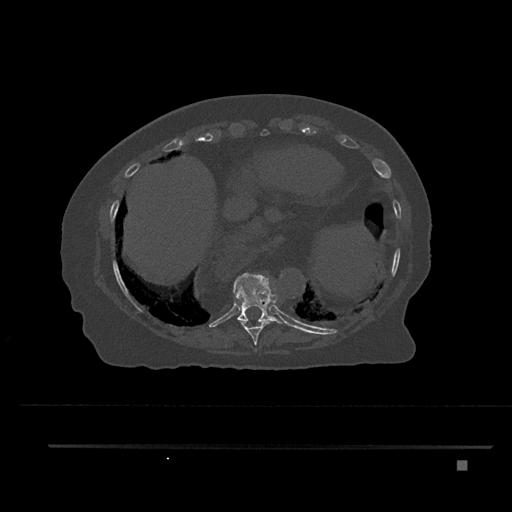
CT including the spine, one axial slice. Slice 376 of 797 in the series (ordered by position). Bone window (W 1800 / L 400 HU). 0.5 mm slice thickness. 512 × 512 image matrix, field of view 437 × 437 mm. Female patient, age 76 years. From the clinical record (not read from this slice): primary cancer: lung.
Outlined on this slice (semi-automatic segmentation, software-assisted and operator-edited):
- T10 vertebra: bounding box (x1, y1, x2, y2) in pixels: (234, 273, 289, 326)
- T9 vertebra: (235, 302, 269, 345)